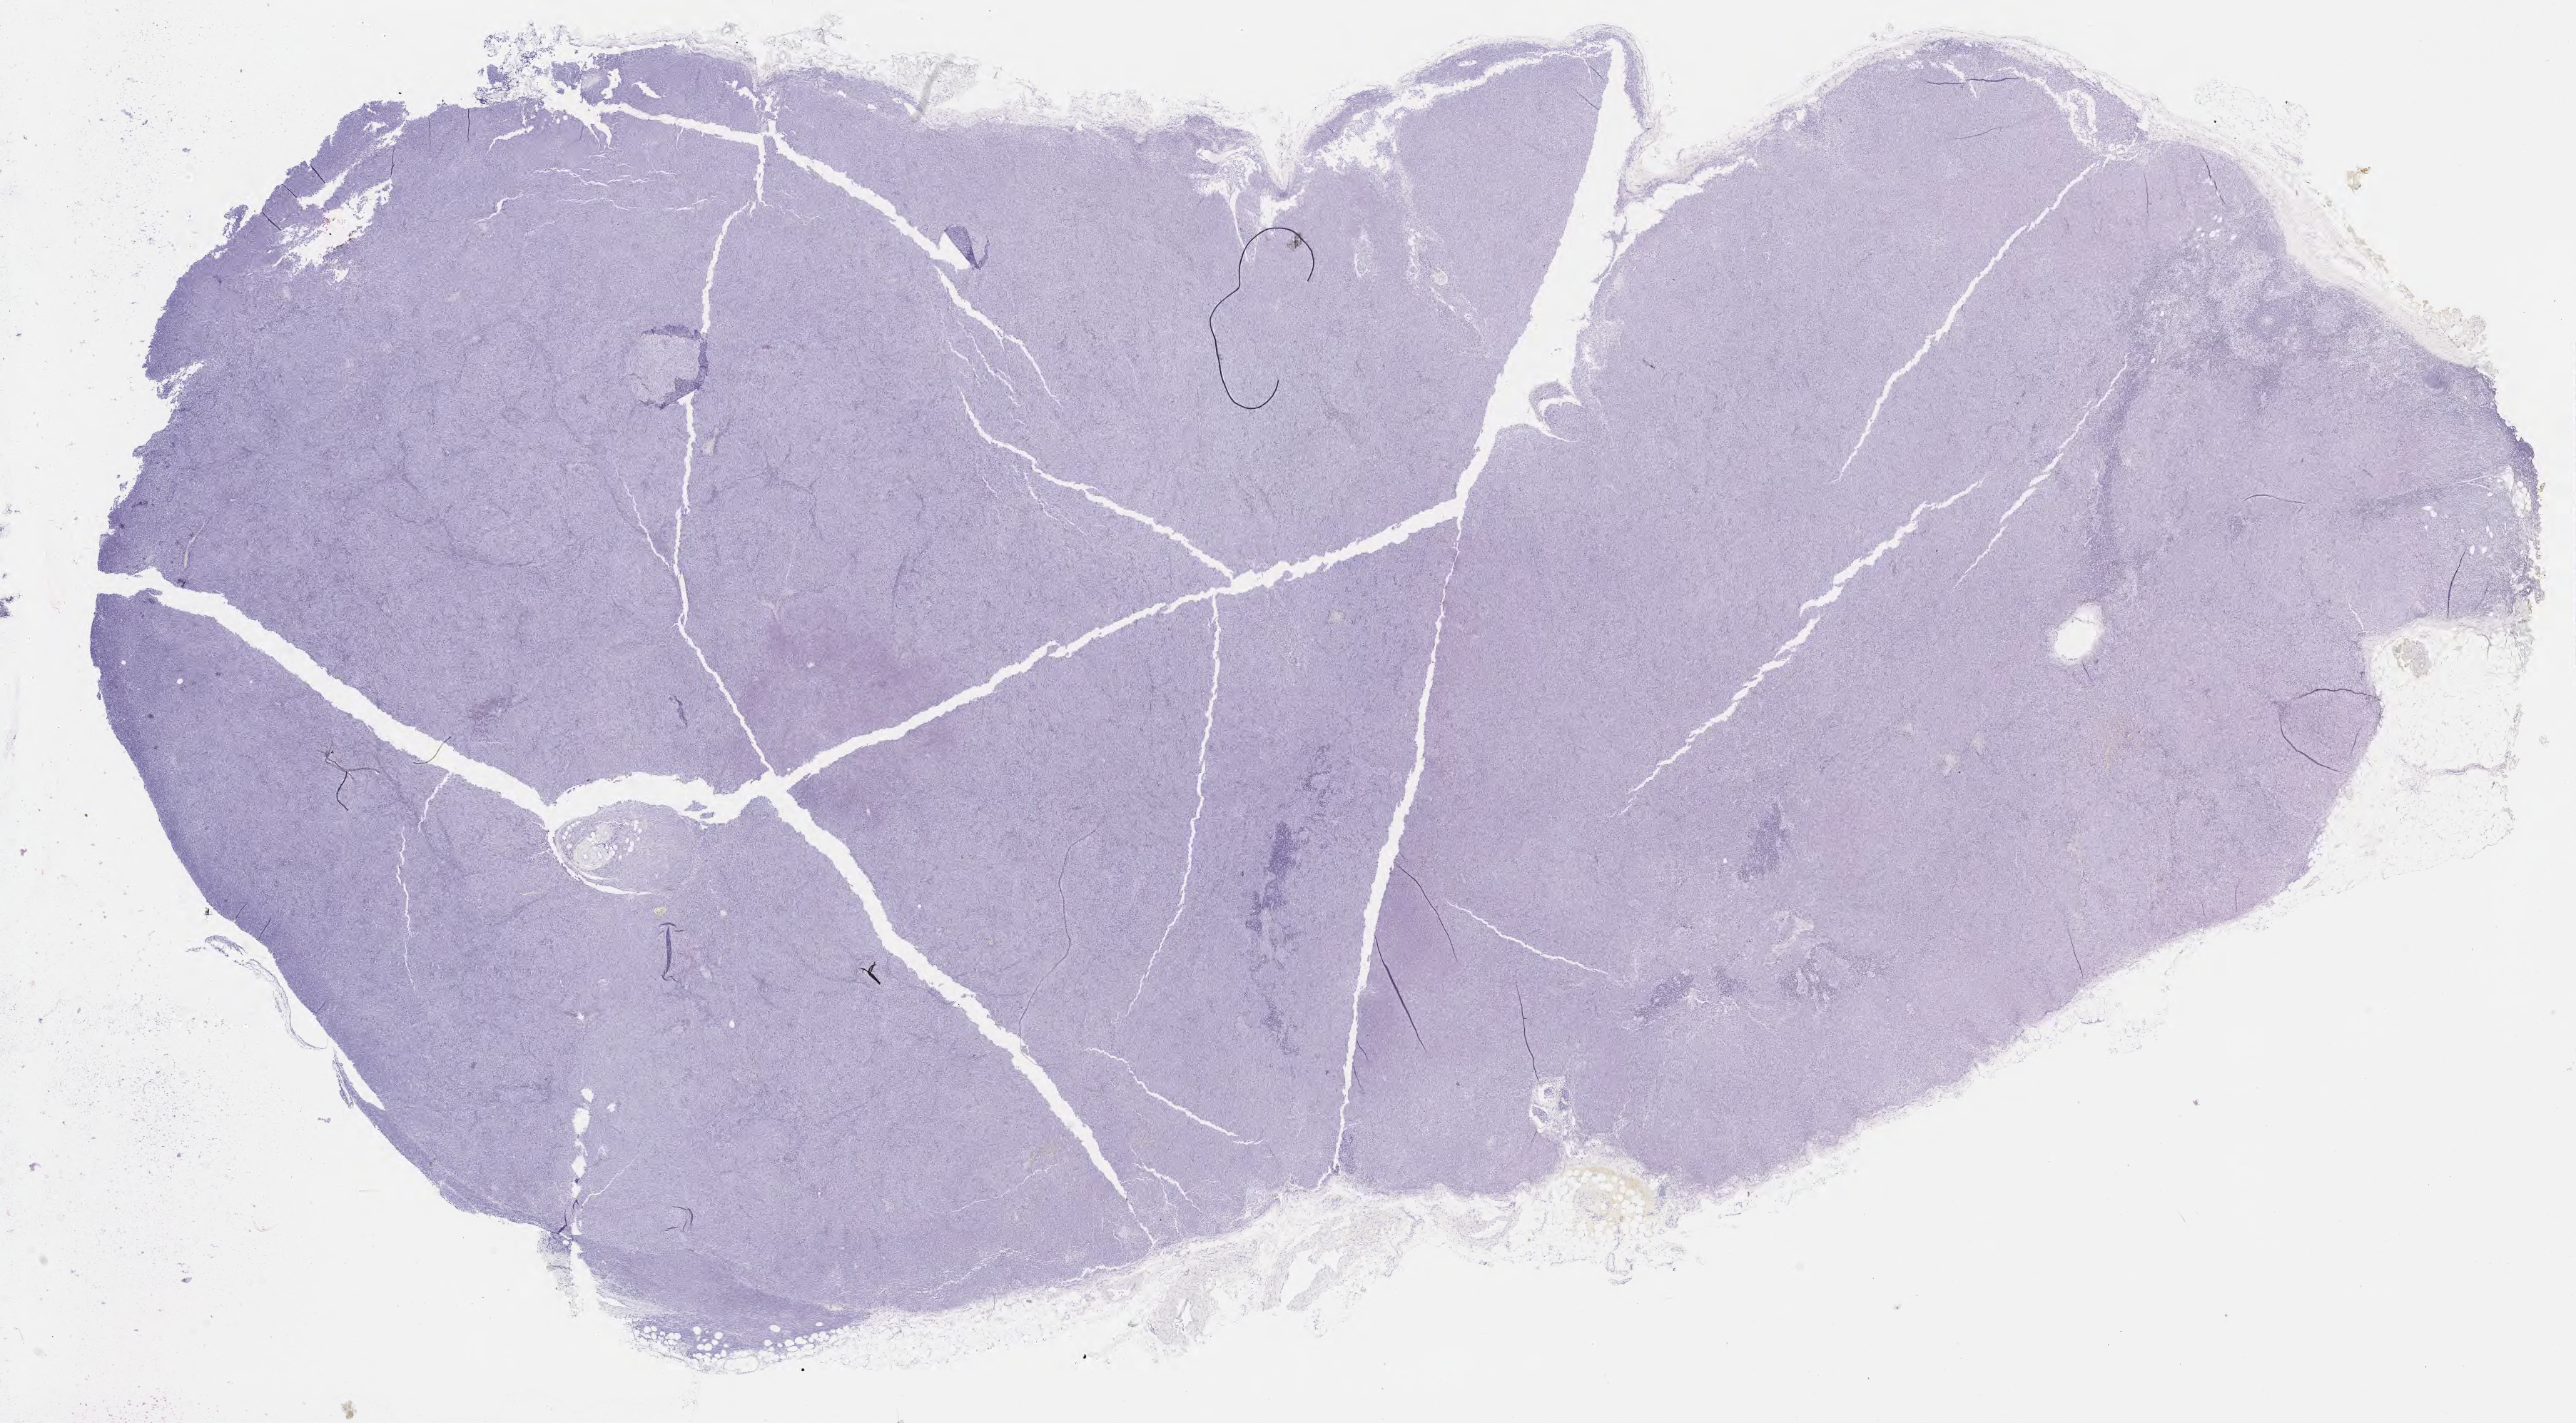
In-situ hybridisation whole-slide image, Epstein–Barr virus-encoded RNA (EBER) probe, a low-resolution overview of the entire scanned area, about 29.2 x 16.1 mm. Tumor tissue. Patient: male, 69 years old.
- diagnosis: Diffuse large B-cell lymphoma, NOS